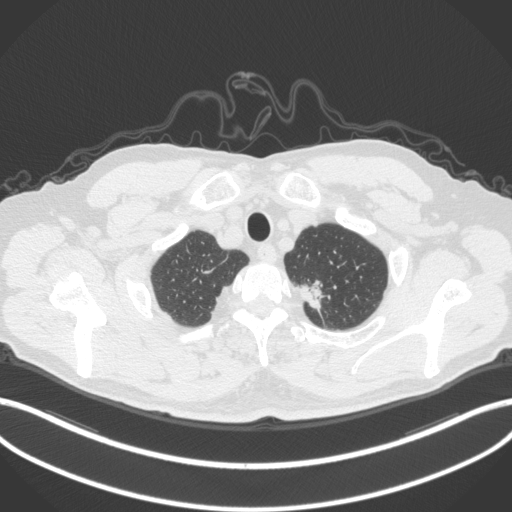
Chest CT, one axial slice. Position 344 of 382 along the scan axis. Lung window (W 1500 / L -600 HU). 1 mm slice thickness. 512 × 512 image matrix, field of view 400 × 400 mm. Patient: male, 64 years. Case-level facts recorded for this patient, not image findings: clinical TNM (as recorded): T1c N0 M0.
Outlined on this slice (rectangle marked by the reading radiologist):
- lung tumour (recorded histology: adenocarcinoma): bounding box <298,276,333,311> (left, top, right, bottom; pixels)